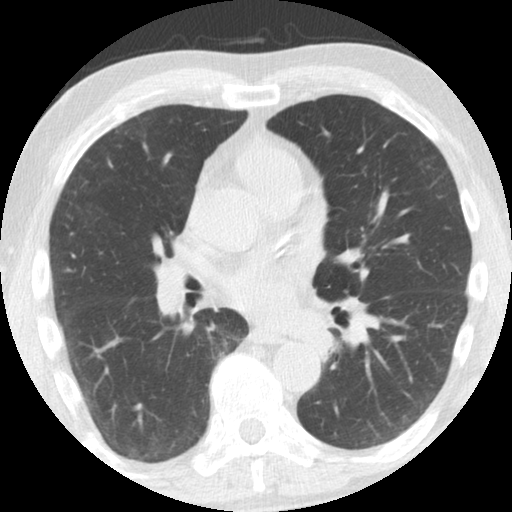
Axial slice from a low-dose chest CT screening exam; third screening round (two years after baseline); lung window (W 1500 / L -600 HU); slice 62 of 108 in the series. Male participant, aged 61 years at enrolment. Former smoker at enrolment.
Expert-annotated lung lesion, box from (x=296, y=316) to (x=345, y=362) px. No non-calcified nodule or mass ≥4 mm was recorded by the screening reader at this exam. Official screen result: negative screen, minor abnormalities not suspicious for lung cancer. Lung cancer was diagnosed 363 days after this screen: squamous cell carcinoma, NOS, left upper lobe, left lower lobe, well differentiated (G1), stage IIB (AJCC 6th edition), 100 mm at pathology.